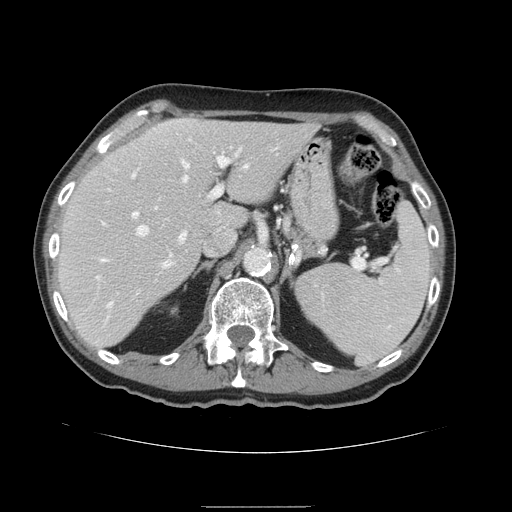
Contrast-enhanced abdominal CT, one axial slice; slice 101 of 168 in the series (ordered by position); 120 kVp; intravenous contrast given; soft-tissue window (W 400 / L 40 HU); 2.5 mm slice thickness; 512 × 512 image matrix, field of view 386 × 386 mm. Male patient, age 74 years. From the clinical record (not read from this slice): diagnosis: colorectal cancer liver metastases, imaged before liver resection; multiple liver metastases: no; largest metastasis: 14.5 cm; disease in both lobes: yes.
Outlined on this slice (outlined manually by an expert reader):
- hepatic veins: bounding box [x1, y1, x2, y2] px = [103, 161, 248, 306]
- liver: [57, 118, 319, 347]
- planned liver remnant (the part of the liver to remain after resection): [57, 118, 319, 348]
- portal vein (with intrahepatic branches): [105, 157, 230, 243]